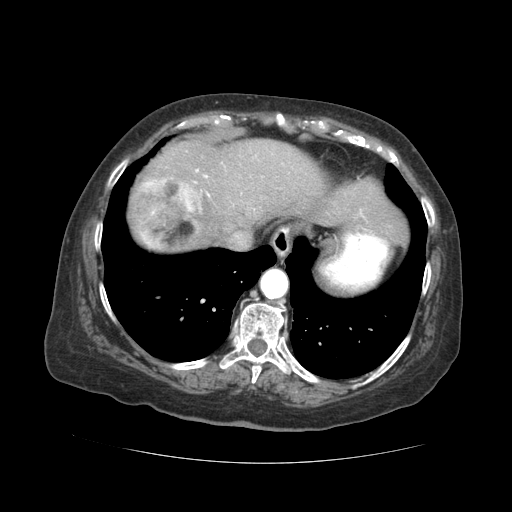
Contrast-enhanced abdominal CT (liver protocol), one axial slice. 120 kVp. Soft-tissue window (W 400 / L 40 HU). 2.5 mm slice thickness. 512 × 512 image matrix. From the clinical record (not read from this slice): diagnosis: hepatocellular carcinoma (patient treated with transarterial chemoembolisation; whether this scan precedes or follows treatment is not stated here); TNM stage (as recorded): Stage-I; Child-Pugh class: A; tumour nodularity: uninodular.
Outlined on this slice (semi-automatic segmentation, software-assisted and operator-edited):
- liver parenchyma outside the tumour (the mass and vessels are separate outlines, so this box may not span the whole liver): box from (x=128, y=138) to (x=406, y=252) px
- mass: (x=137, y=177)–(x=201, y=248)
- liver vessels: (x=142, y=169)–(x=210, y=245)